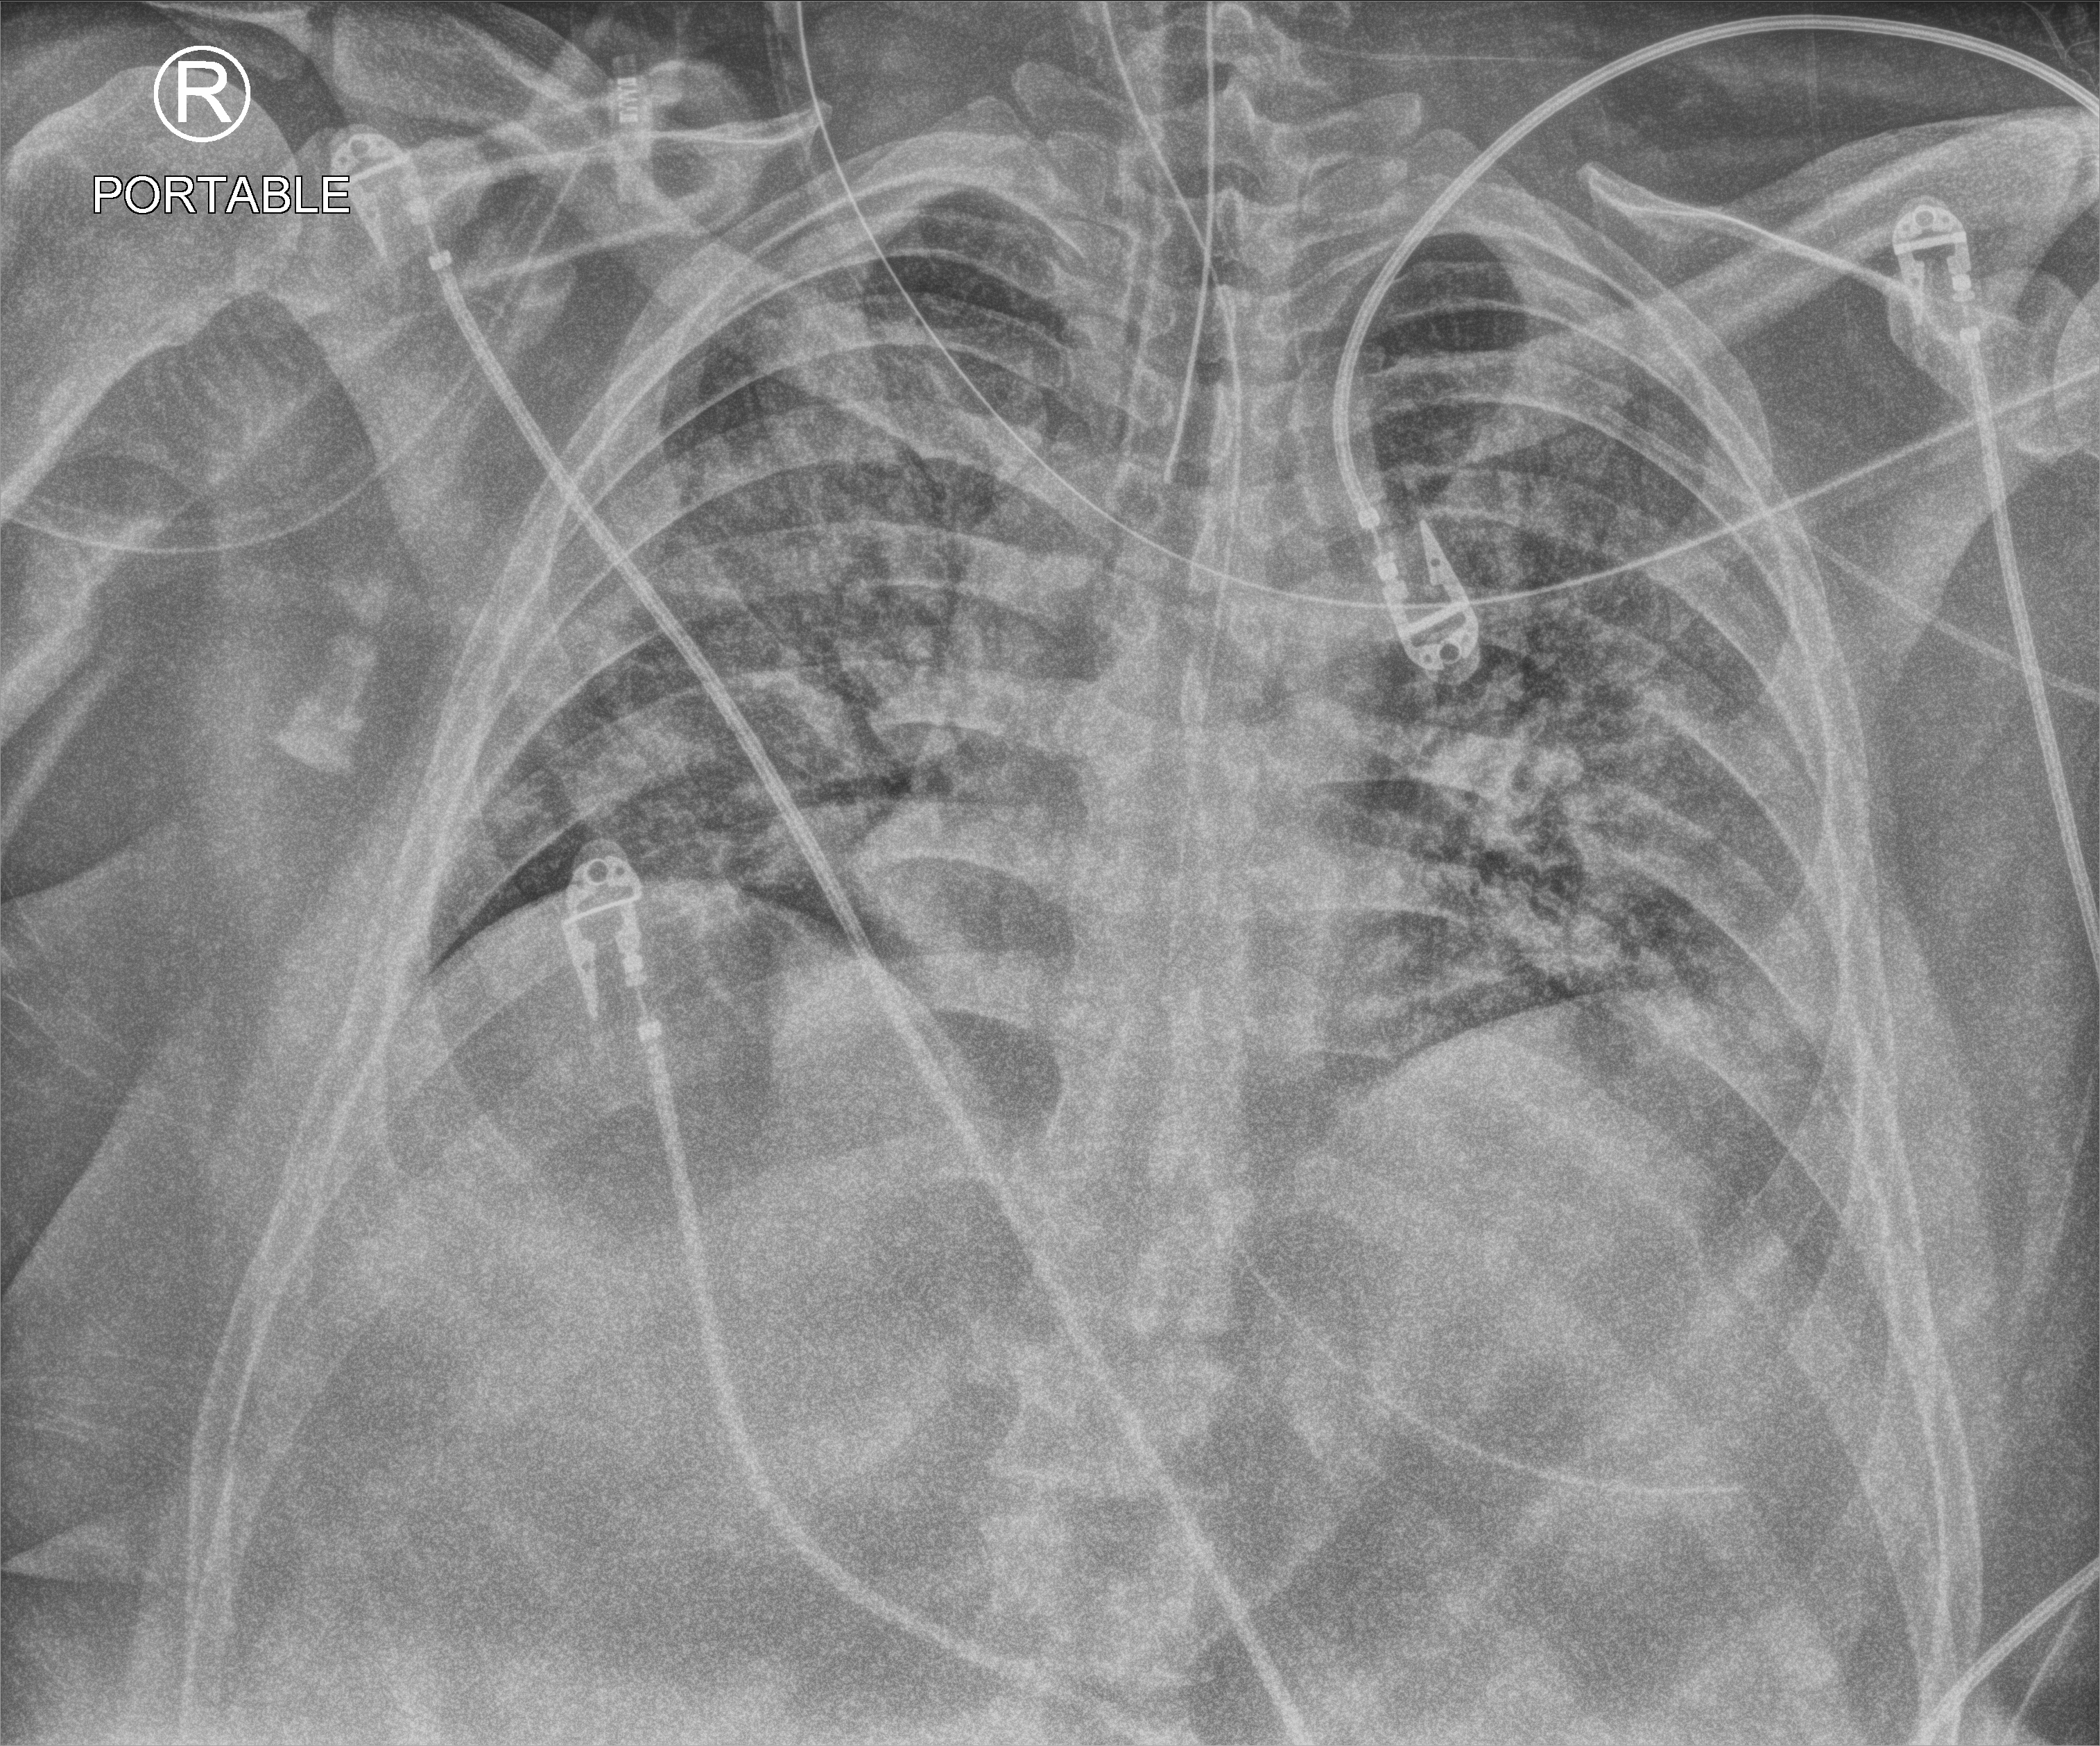
Chest X-ray (portable); anteroposterior (AP) projection. Patient hospitalised with COVID-19, aged 18–59 years.
Hospital-stay facts (about this admission, not read from this image; timing relative to this image not recorded):
- COPD (admission record): no